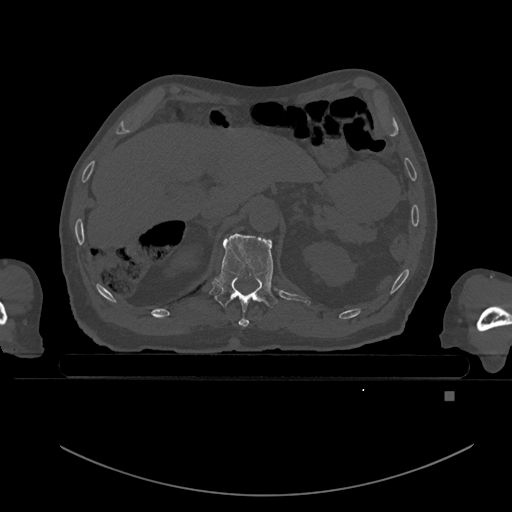
CT including the spine, one axial slice. Position 31 of 969 along the scan axis. Bone window (W 1800 / L 400 HU). 0.5 mm slice thickness. 512 × 512 image matrix, field of view 456 × 456 mm. Patient: male, 82 years. From the clinical record (not read from this slice): primary cancer: prostate; vertebrae with lytic lesions (as recorded): T11, T9, T8, T2.
Outlined on this slice (semi-automatically segmented with operator editing):
- T11 vertebra: bounding box [x1, y1, x2, y2] px = [214, 233, 278, 327]